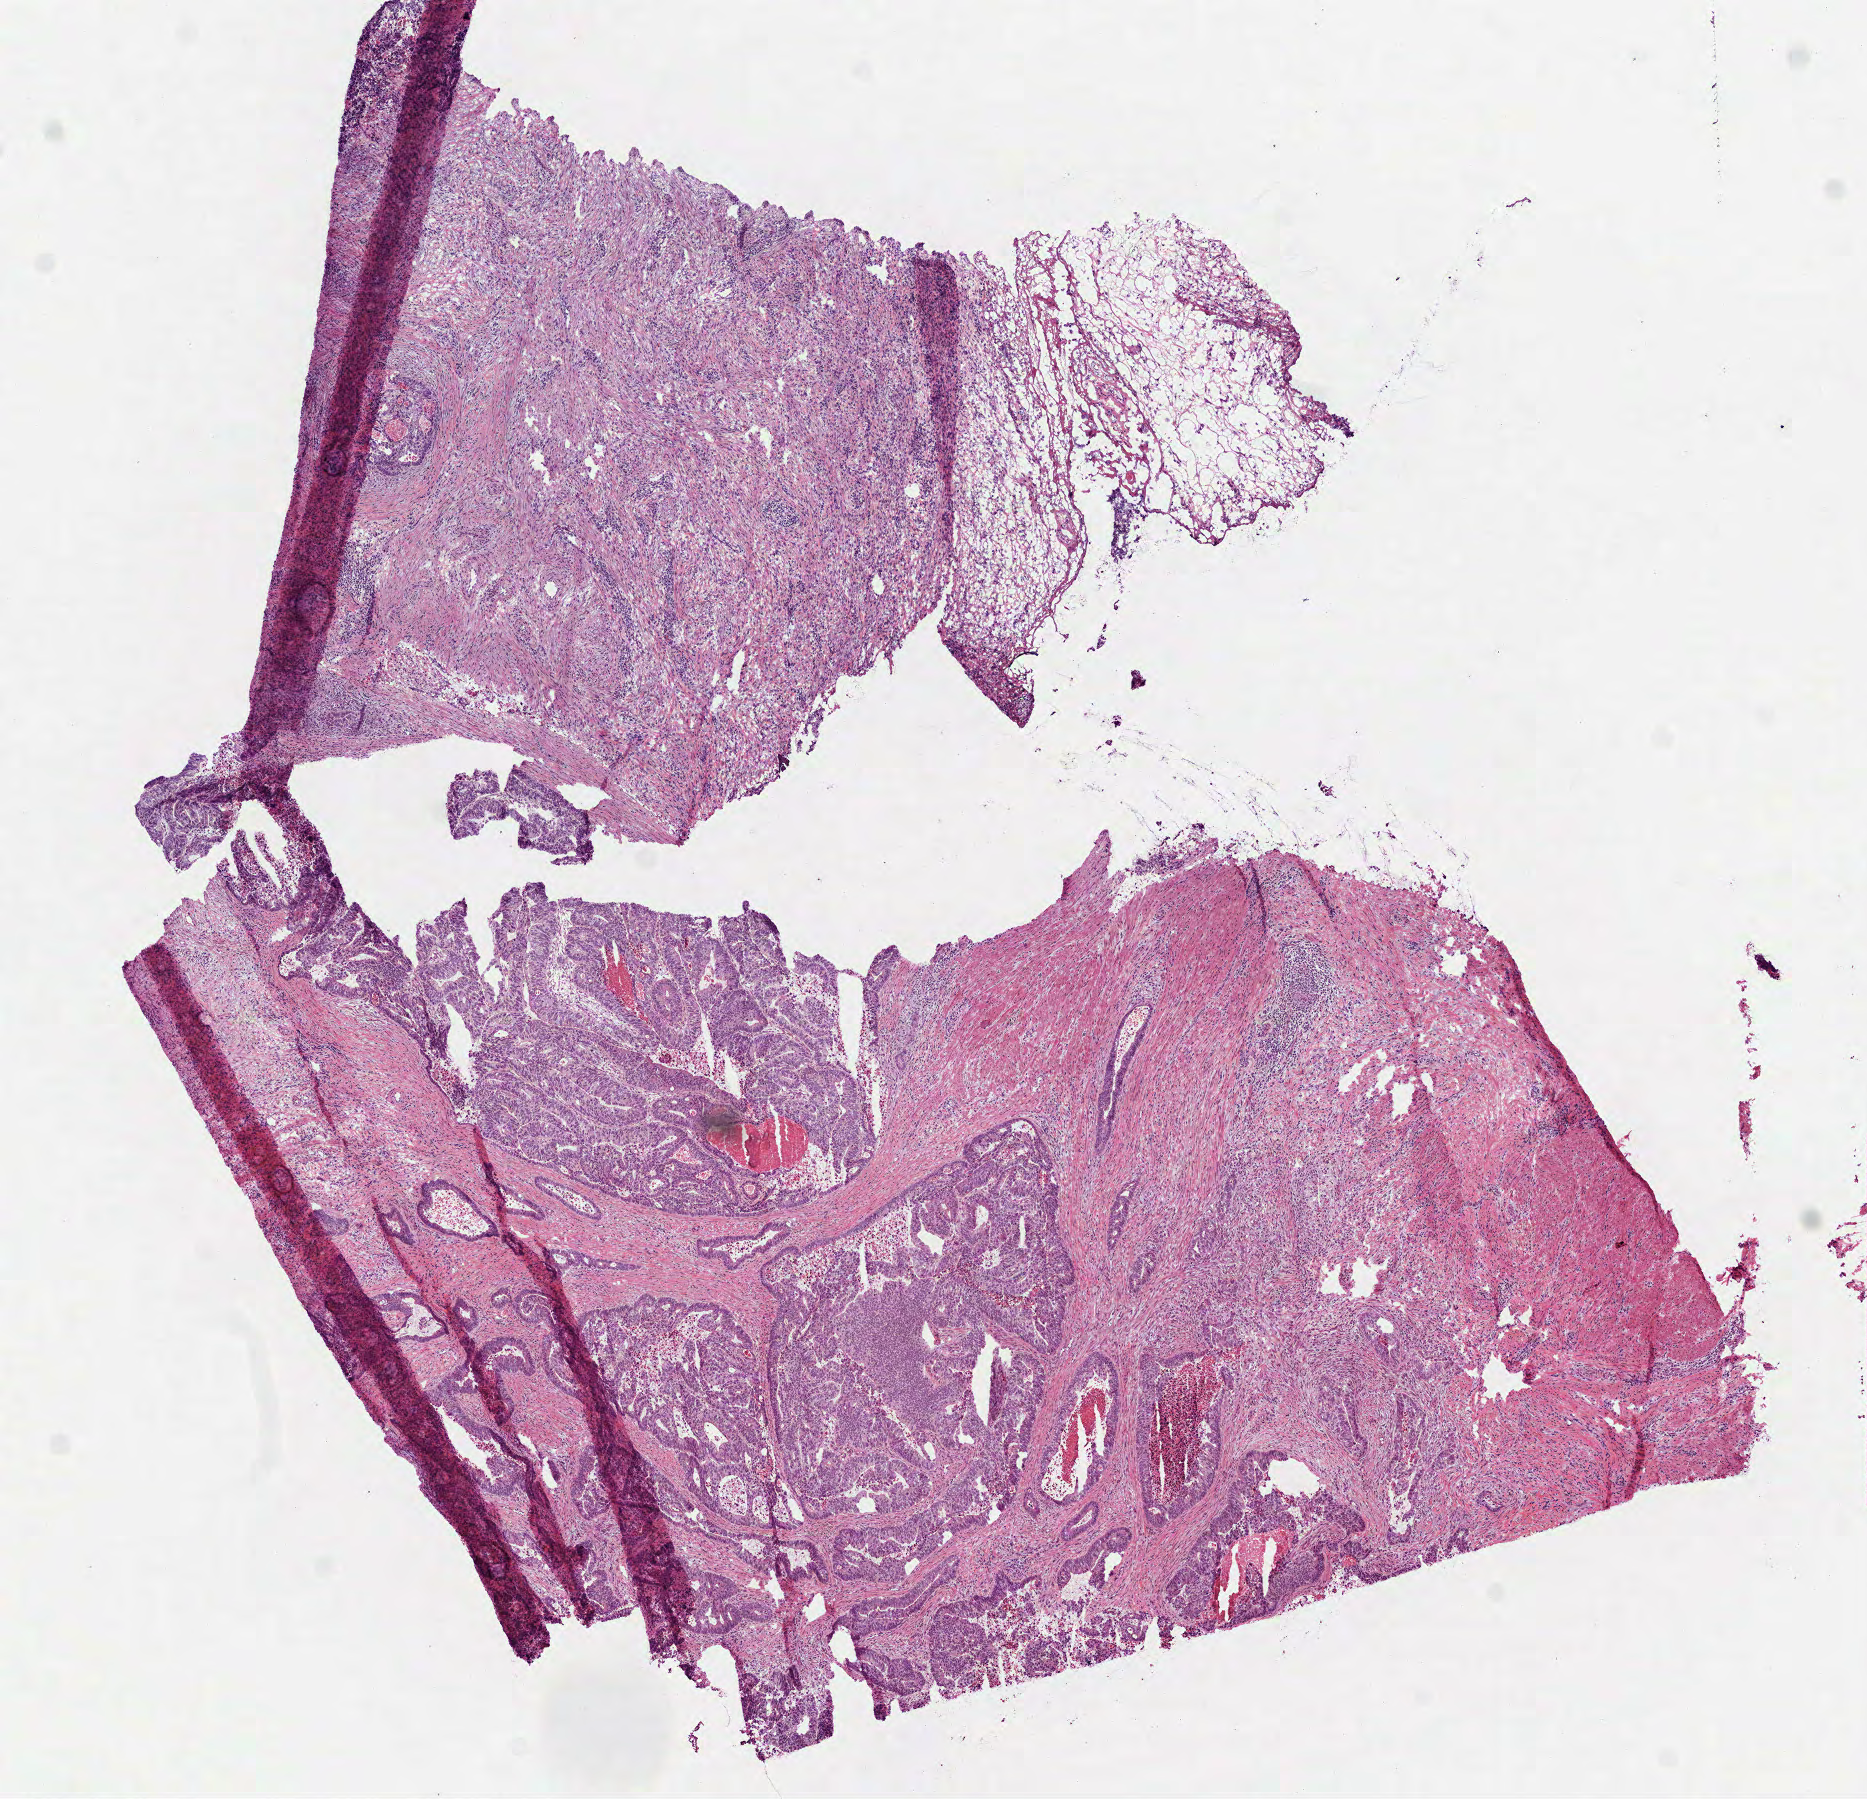
H&E-stained whole-slide image — whole scanned area (about 7.5 x 7.3 mm) shown as a low-resolution overview, frozen section, colon, primary tumour sample. Female patient; age at initial diagnosis 55 years. Pathologist review of this section (percent, as recorded): tumour cells 50%, tumour nuclei 60%, normal cells 40%, stromal cells 0%, necrosis 10%. Infiltration values recorded for this section: lymphocyte infiltration 20%, monocyte infiltration 2%, neutrophil infiltration 0%.
• TNM: T3 N1b MX
• lymph nodes positive (case pathology): 2 of 33 examined
• AJCC pathologic stage: IIIB
• histologic diagnosis: Adenocarcinoma, NOS